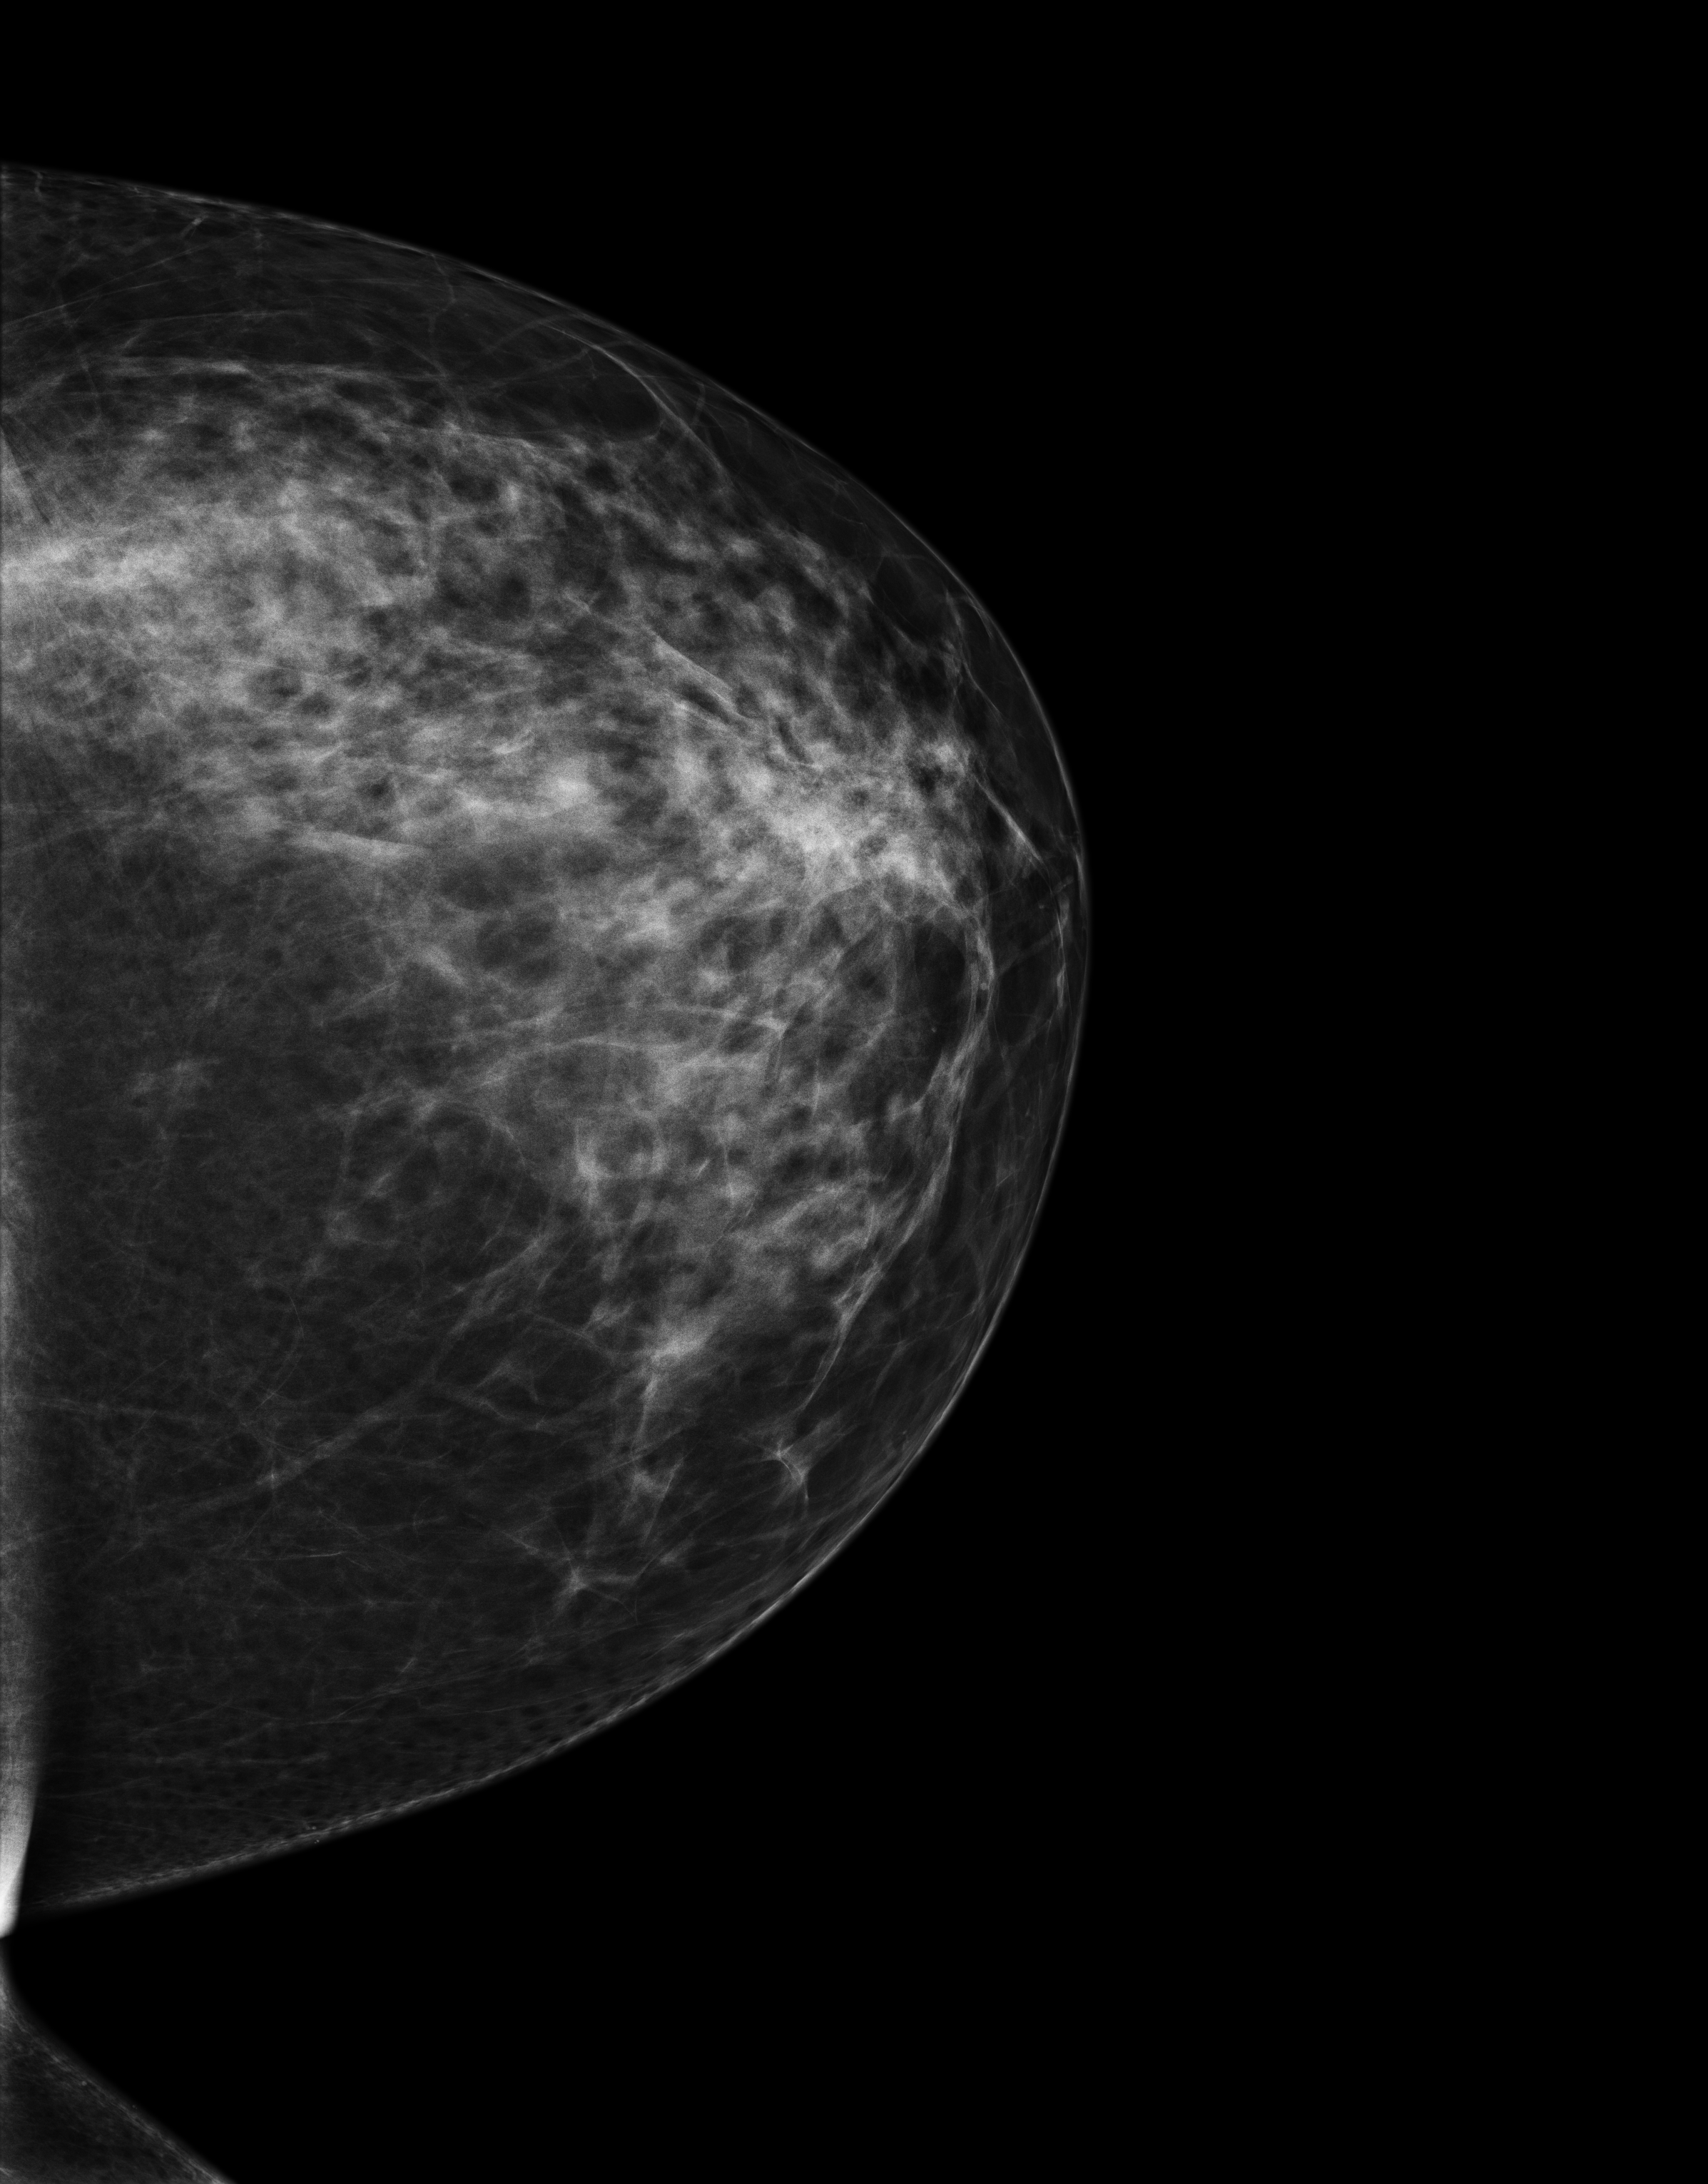
Screening examination, compressed breast thickness 77 mm. Patient: female, 43 years.
Image type: full-field digital mammogram. Breast: left. Projection: cranio-caudal projection.